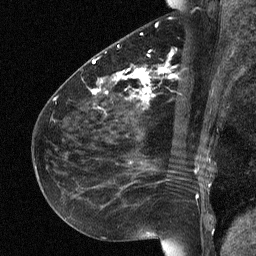
Breast MRI (dynamic contrast-enhanced), one sagittal slice; slice 29 of 64 in the series (ordered by position); dynamic contrast-enhanced study with each time point stored as its own series, time point 2 of 3 at this slice position (early post-contrast, ordered by acquisition time); 1.5 T; TE 4.8 ms, TR 27 ms; 256 × 256 image matrix, field of view 180 × 180 mm. Female patient, age 51 years. Case-level facts recorded for this patient, not image findings: setting: breast cancer imaged before/during neoadjuvant chemotherapy; receptor status: HR-positive, HER2-negative.
Annotated regions visible in this slice (semi-automatically segmented with operator editing):
- analysis volume of interest (the breast-tissue region the enhancement analysis was run in; not a lesion): bounding box [x1, y1, x2, y2] px = [72, 34, 182, 118]
- tumour enhancement mask (voxels above the 90 % enhancement threshold inside the analysis volume of interest): [92, 60, 173, 102]